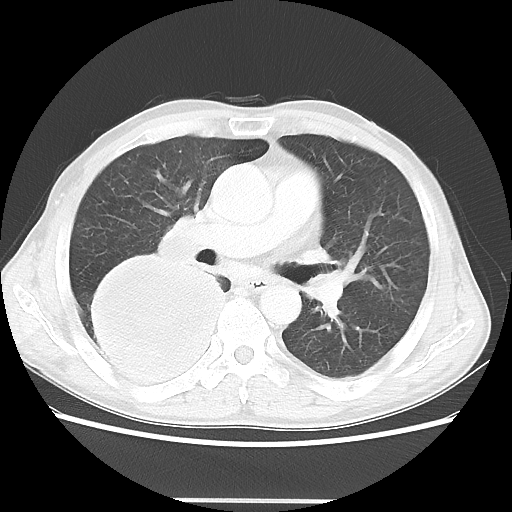
Chest CT, one axial slice; slice 27 of 48 in the series (ordered by position); reconstruction kernel LUNG; 100 kVp; lung window (W 1500 / L -600 HU); 5 mm slice thickness; 512 × 512 image matrix, field of view 361 × 361 mm. Male patient, age 66 years. Case-level facts recorded for this patient, not image findings: clinical TNM (as recorded): T4 N1 M1.
Structures marked on this image (bounding box drawn by a radiologist):
- lung tumour (recorded histology: small cell carcinoma): box from (x=70, y=244) to (x=234, y=403) px